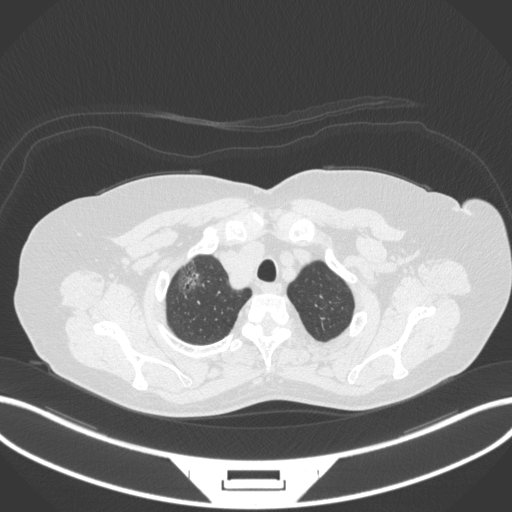
Chest CT, one axial slice; position 311 of 365 along the scan axis; 120 kVp; lung window (W 1500 / L -600 HU); 512 × 512 image matrix. Female patient, age 62 years. From the clinical record (not read from this slice): clinical TNM (as recorded): T1c N0 M0.
Outlined on this slice (rectangle marked by the reading radiologist):
- lung tumour (recorded histology: adenocarcinoma): bounding box (x1, y1, x2, y2) in pixels: (175, 259, 206, 300)